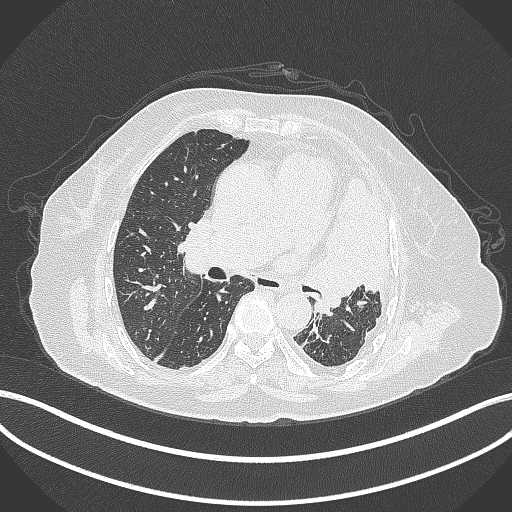
Chest CT, one axial slice; position 210 of 399 along the scan axis; lung window (W 1500 / L -600 HU); 1 mm slice thickness; 512 × 512 image matrix, field of view 400 × 400 mm. Female patient, age 75 years. From the clinical record (not read from this slice): clinical TNM (as recorded): T3 N3 M1.
Outlined on this slice (rectangle marked by the reading radiologist):
- lung tumour (recorded histology: adenocarcinoma): bounding box (x1, y1, x2, y2) in pixels: (298, 168, 398, 312)